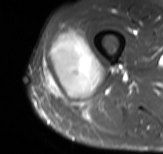
MRI of an extremity soft-tissue mass, one axial slice; position 32 of 61 along the scan axis; STIR; MR volume resampled by the dataset authors to the PET/CT grid (not the native acquisition matrix); 3.27 mm slice thickness; 163 × 154 image matrix. Male patient. From the clinical record (not read from this slice): histological type: poorly differentiated synovial sarcoma; grade: high; site of the primary tumour: right buttock.
Structures marked on this image (expert contour drawn on MRI and transferred to this co-registered scan by the dataset authors):
- gross tumour volume including surrounding oedema: box from (x=43, y=27) to (x=102, y=97) px
- gross tumour volume (mass): (x=50, y=32)–(x=102, y=97)